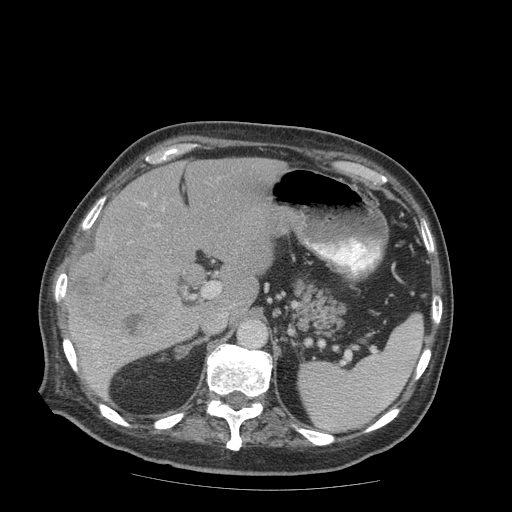
Contrast-enhanced abdominal CT (liver protocol), one axial slice. Slice 52 of 99 in the series (ordered by position). Reconstruction kernel STANDARD. 140 kVp. Soft-tissue window (W 400 / L 40 HU). 2.5 mm slice thickness. 512 × 512 image matrix, field of view 420 × 420 mm. From the clinical record (not read from this slice): diagnosis: hepatocellular carcinoma (patient treated with transarterial chemoembolisation; whether this scan precedes or follows treatment is not stated here); TNM stage (as recorded): Stage-IIIB; Child-Pugh class: A.
Outlined on this slice (semi-automatically segmented with operator editing):
- liver parenchyma outside the tumour (the mass and vessels are separate outlines, so this box may not span the whole liver): box from (x=66, y=158) to (x=286, y=396) px
- mass: (x=68, y=246)–(x=180, y=346)
- liver vessels: (x=98, y=203)–(x=146, y=365)